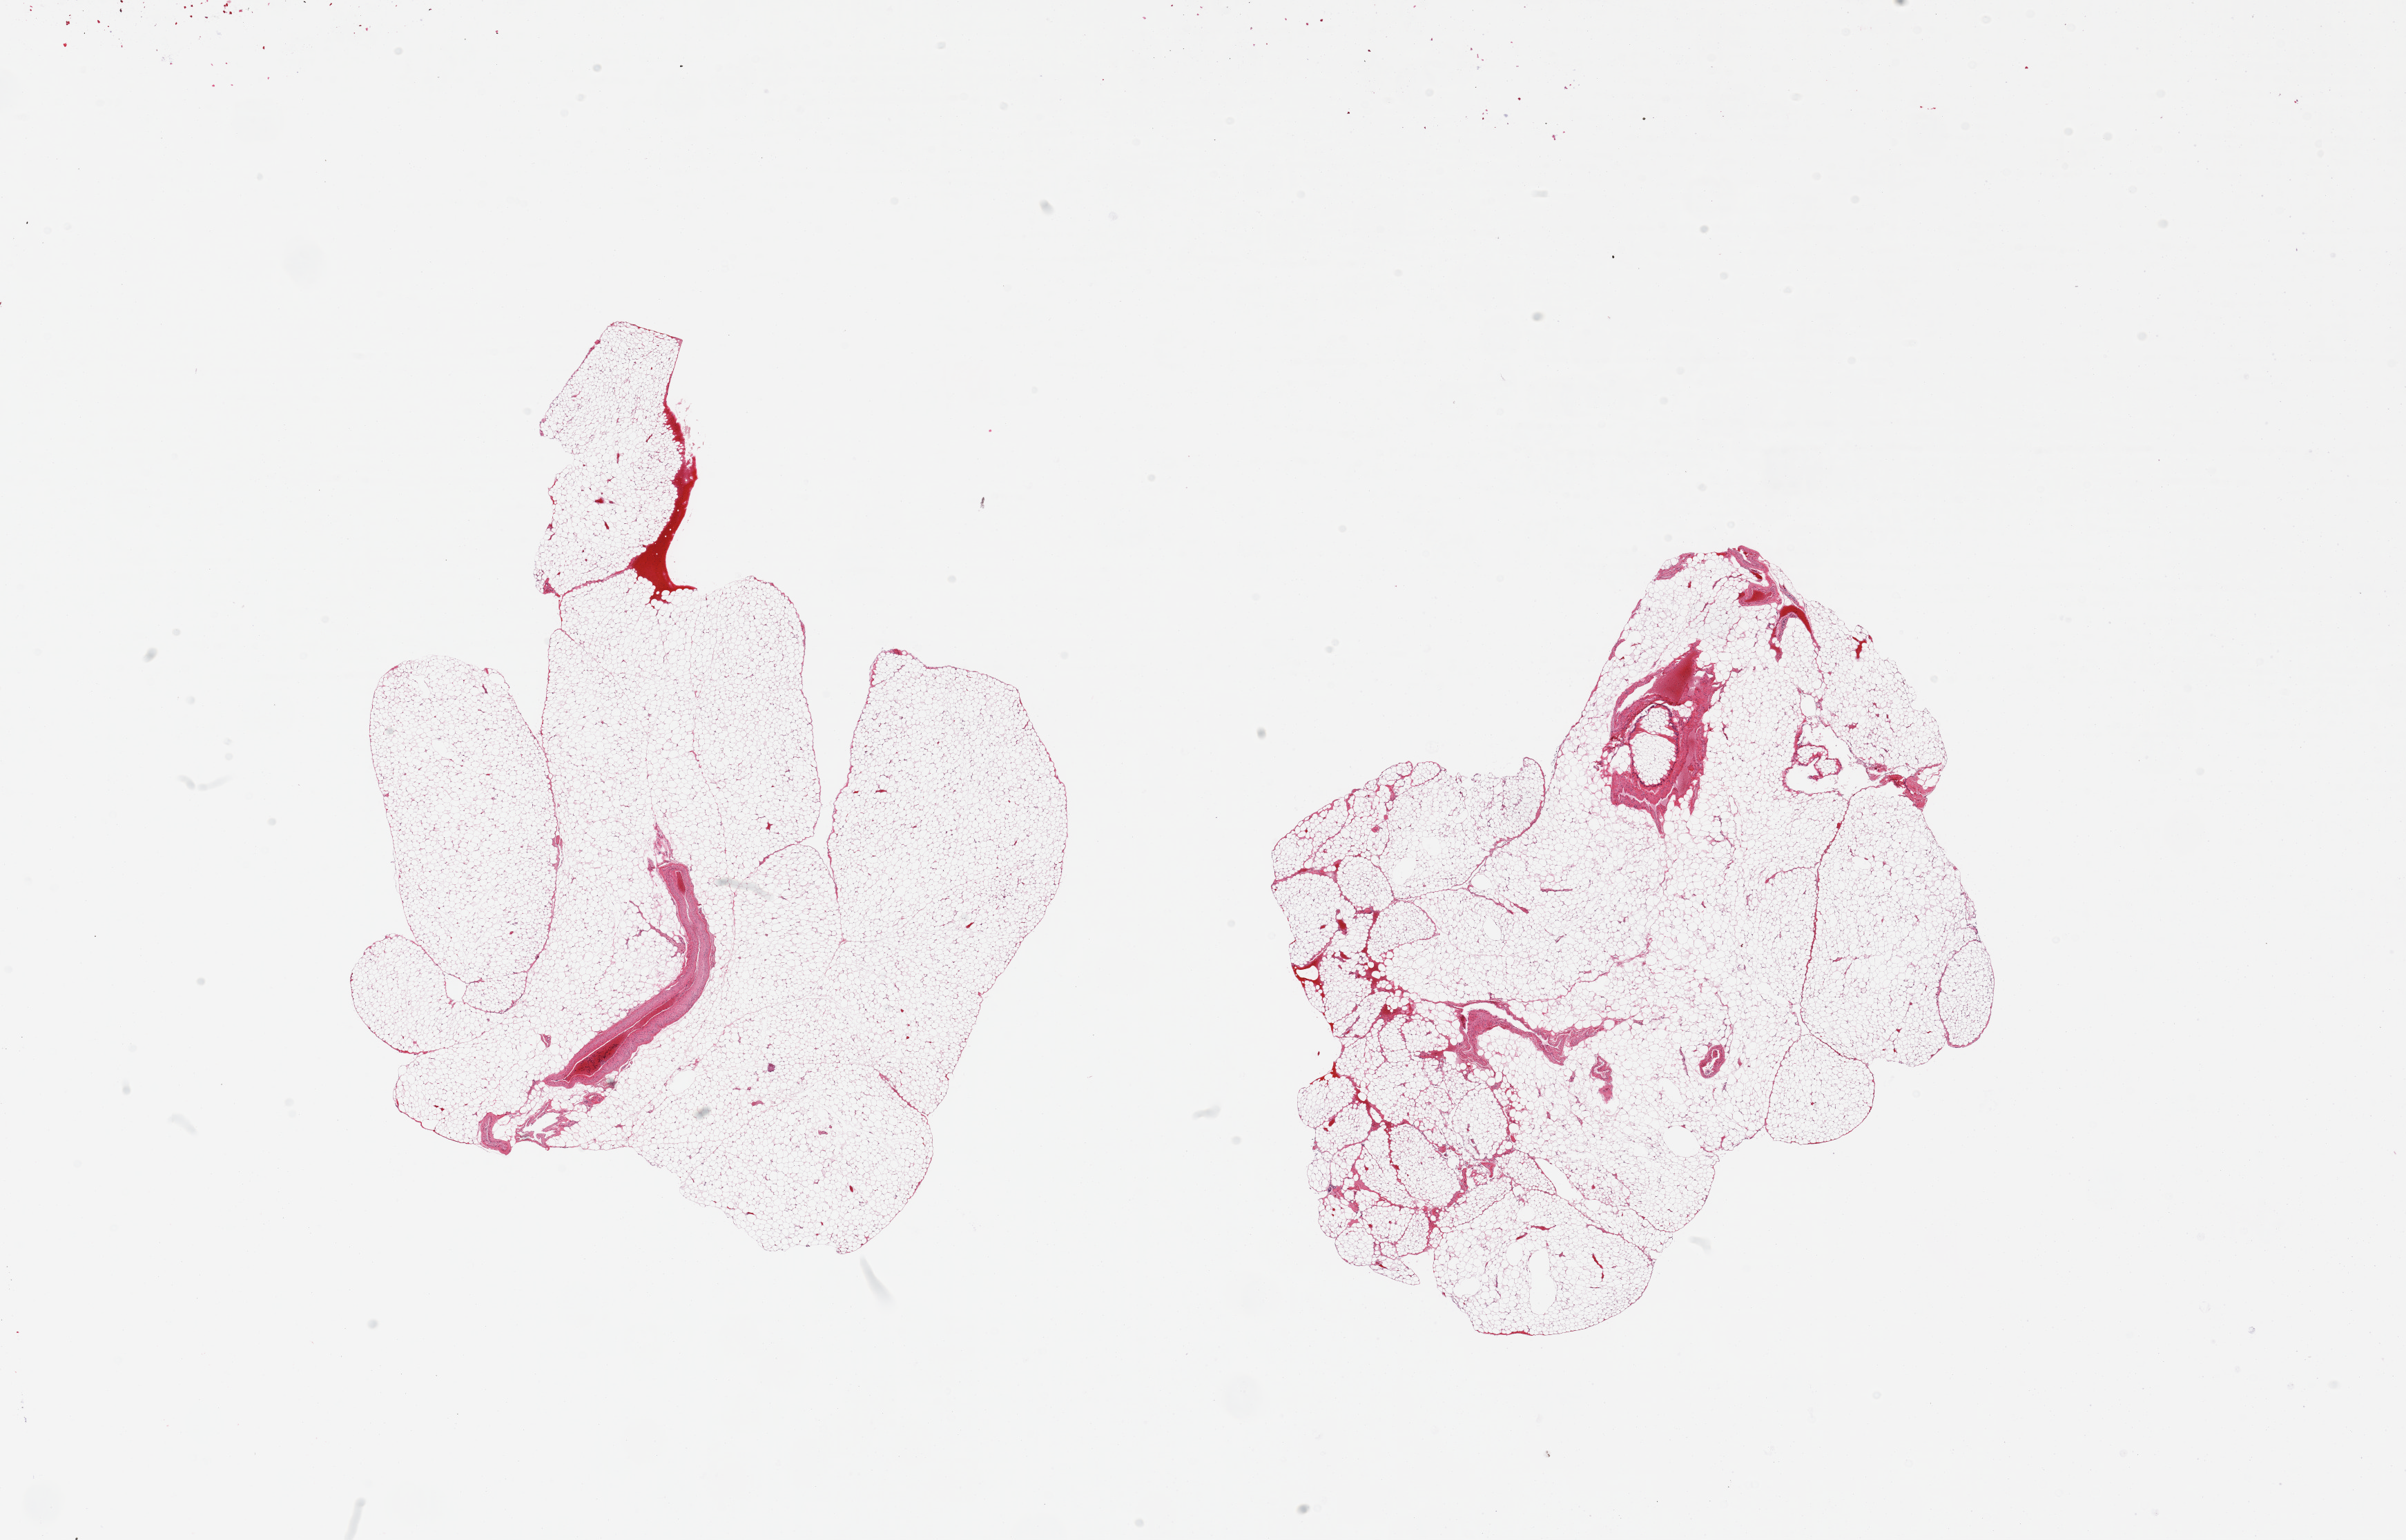
Whole-slide image, hematoxylin and eosin (H&E) stain — a low-resolution overview of the entire scanned area, about 27.6 x 17.6 mm (acquisition: 20x scan), PAXgene-fixed paraffin-embedded (PFPE) section, sampled site (target tissue): omentum, tissue donor sample. Donor: female.
Pathologist's review note for this sample: 2 pieces, ~10% vascular elements/fascia.